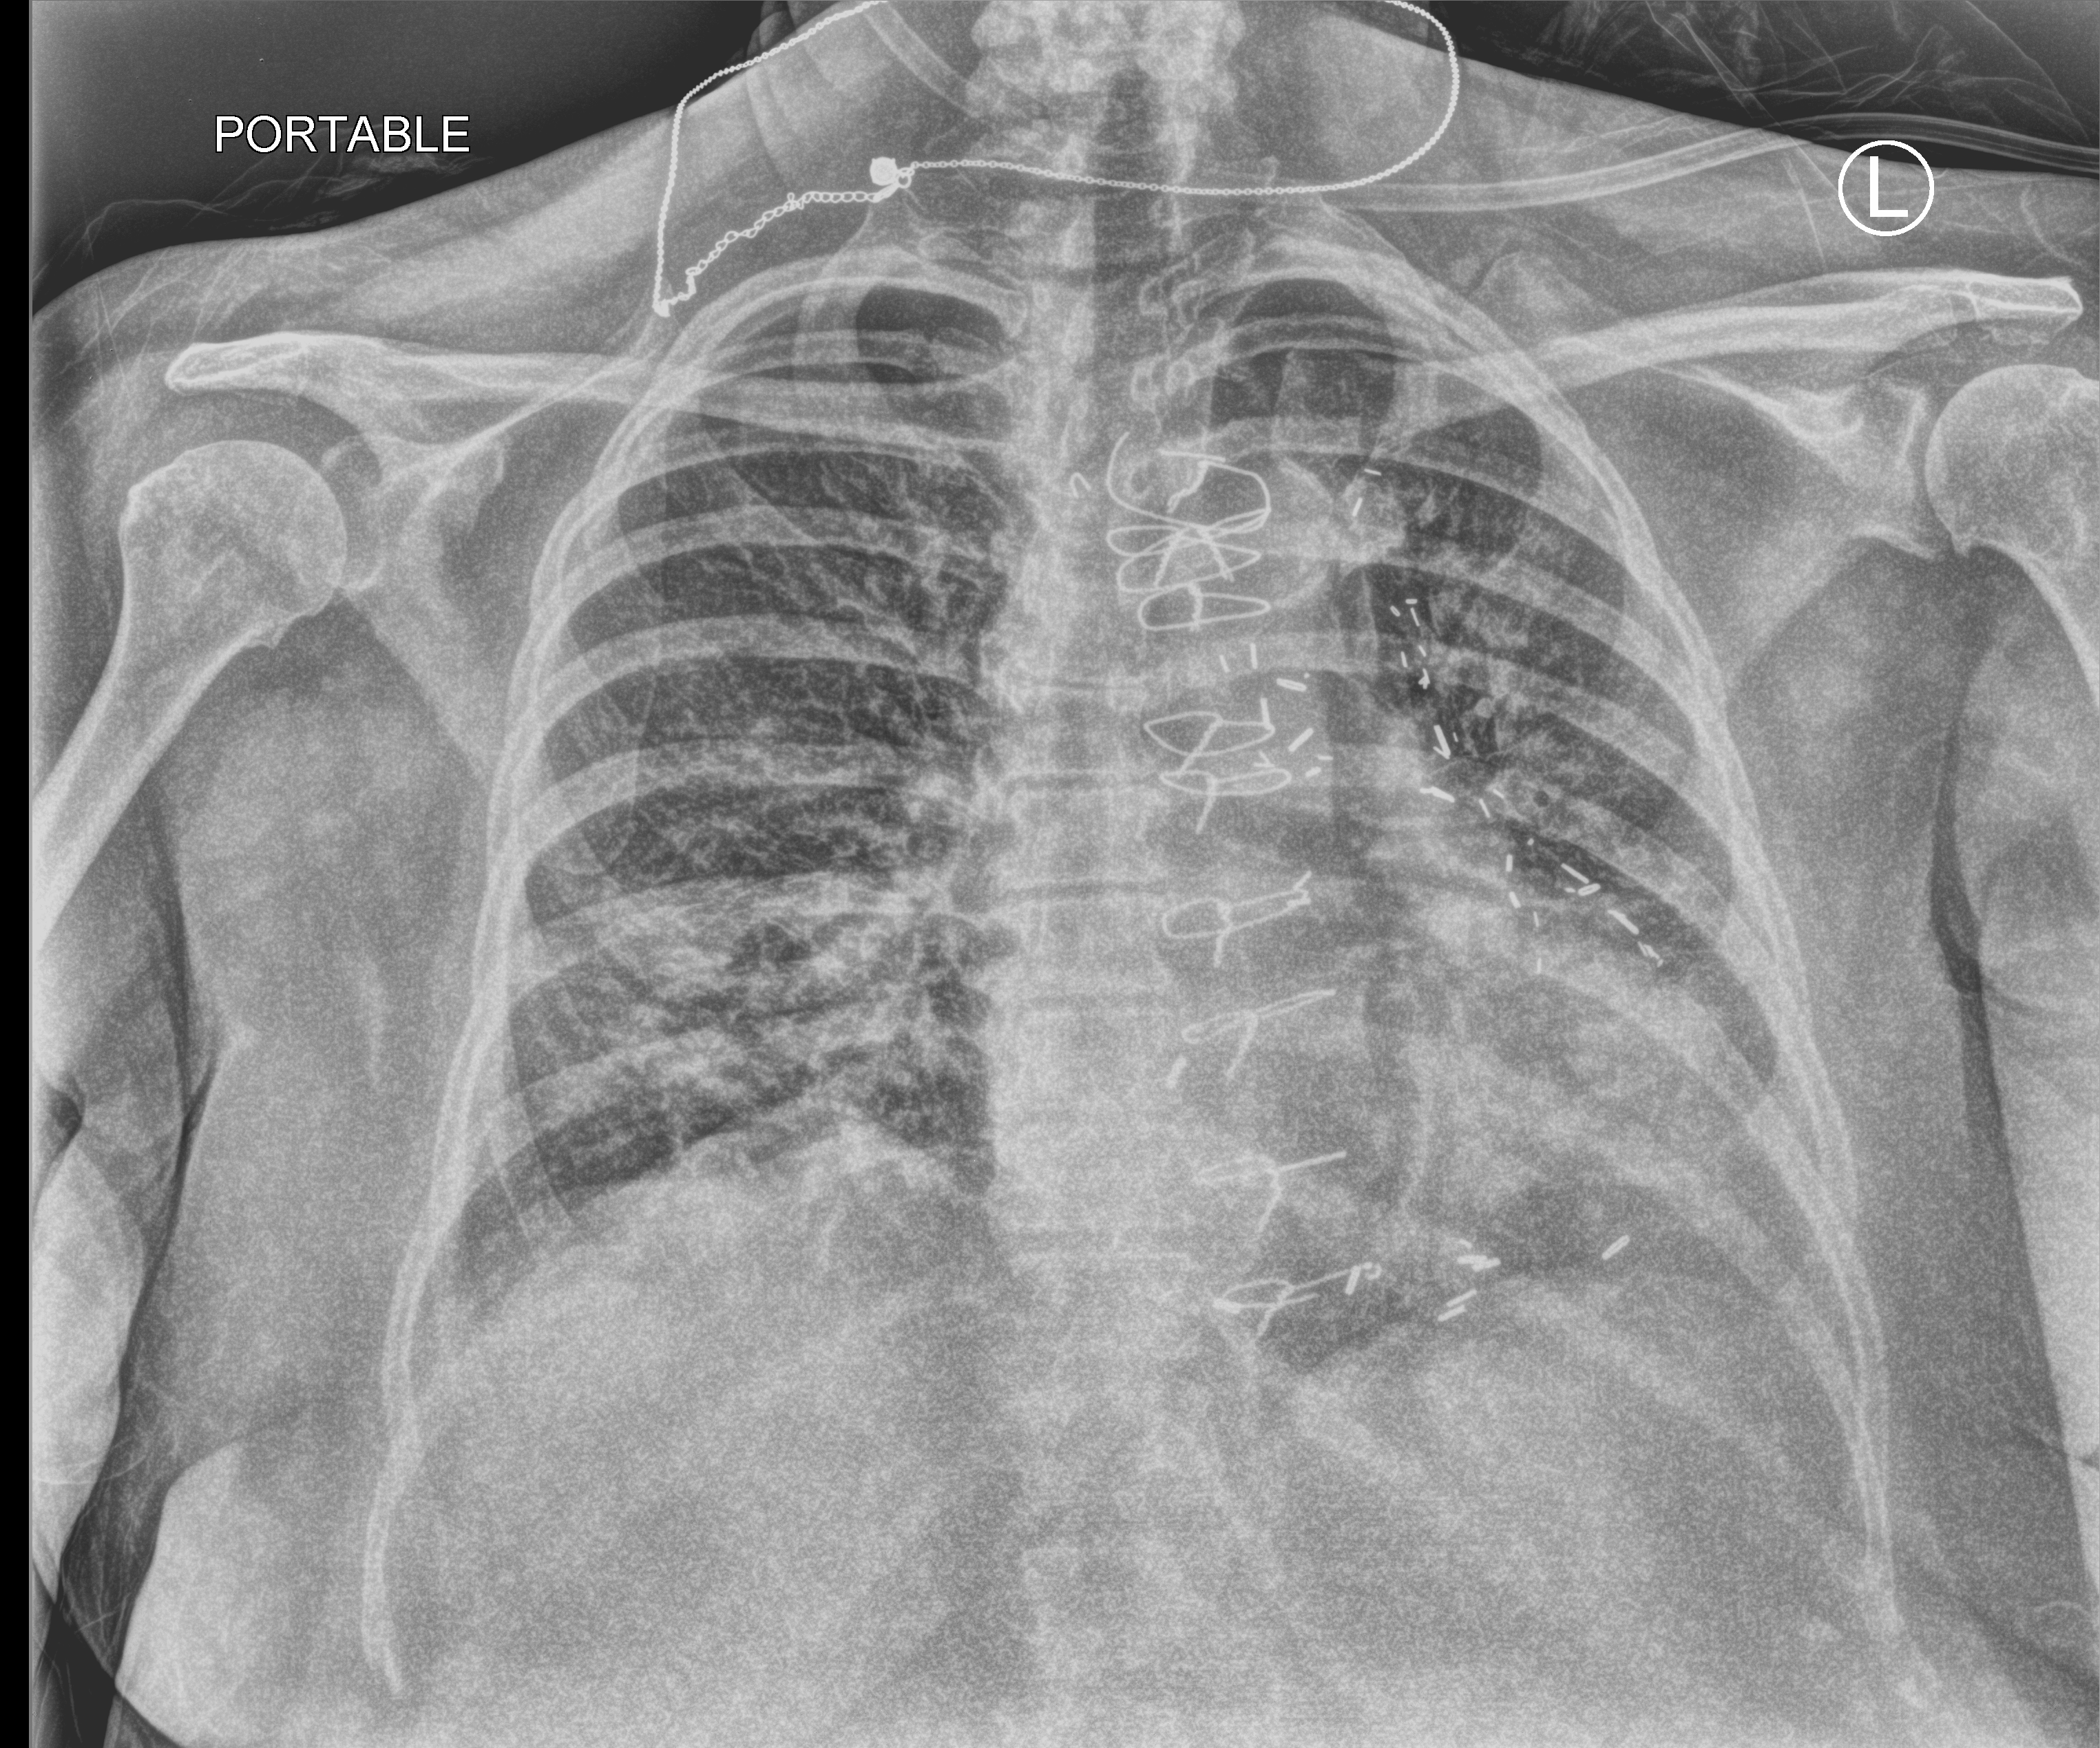
Bedside chest radiograph (computed radiography), anteroposterior (AP) projection. Female patient hospitalised with COVID-19, age 60–74 years.
Hospital-stay facts (about this admission, not read from this image; timing relative to this image not recorded): mechanically ventilated during this hospital stay: yes.